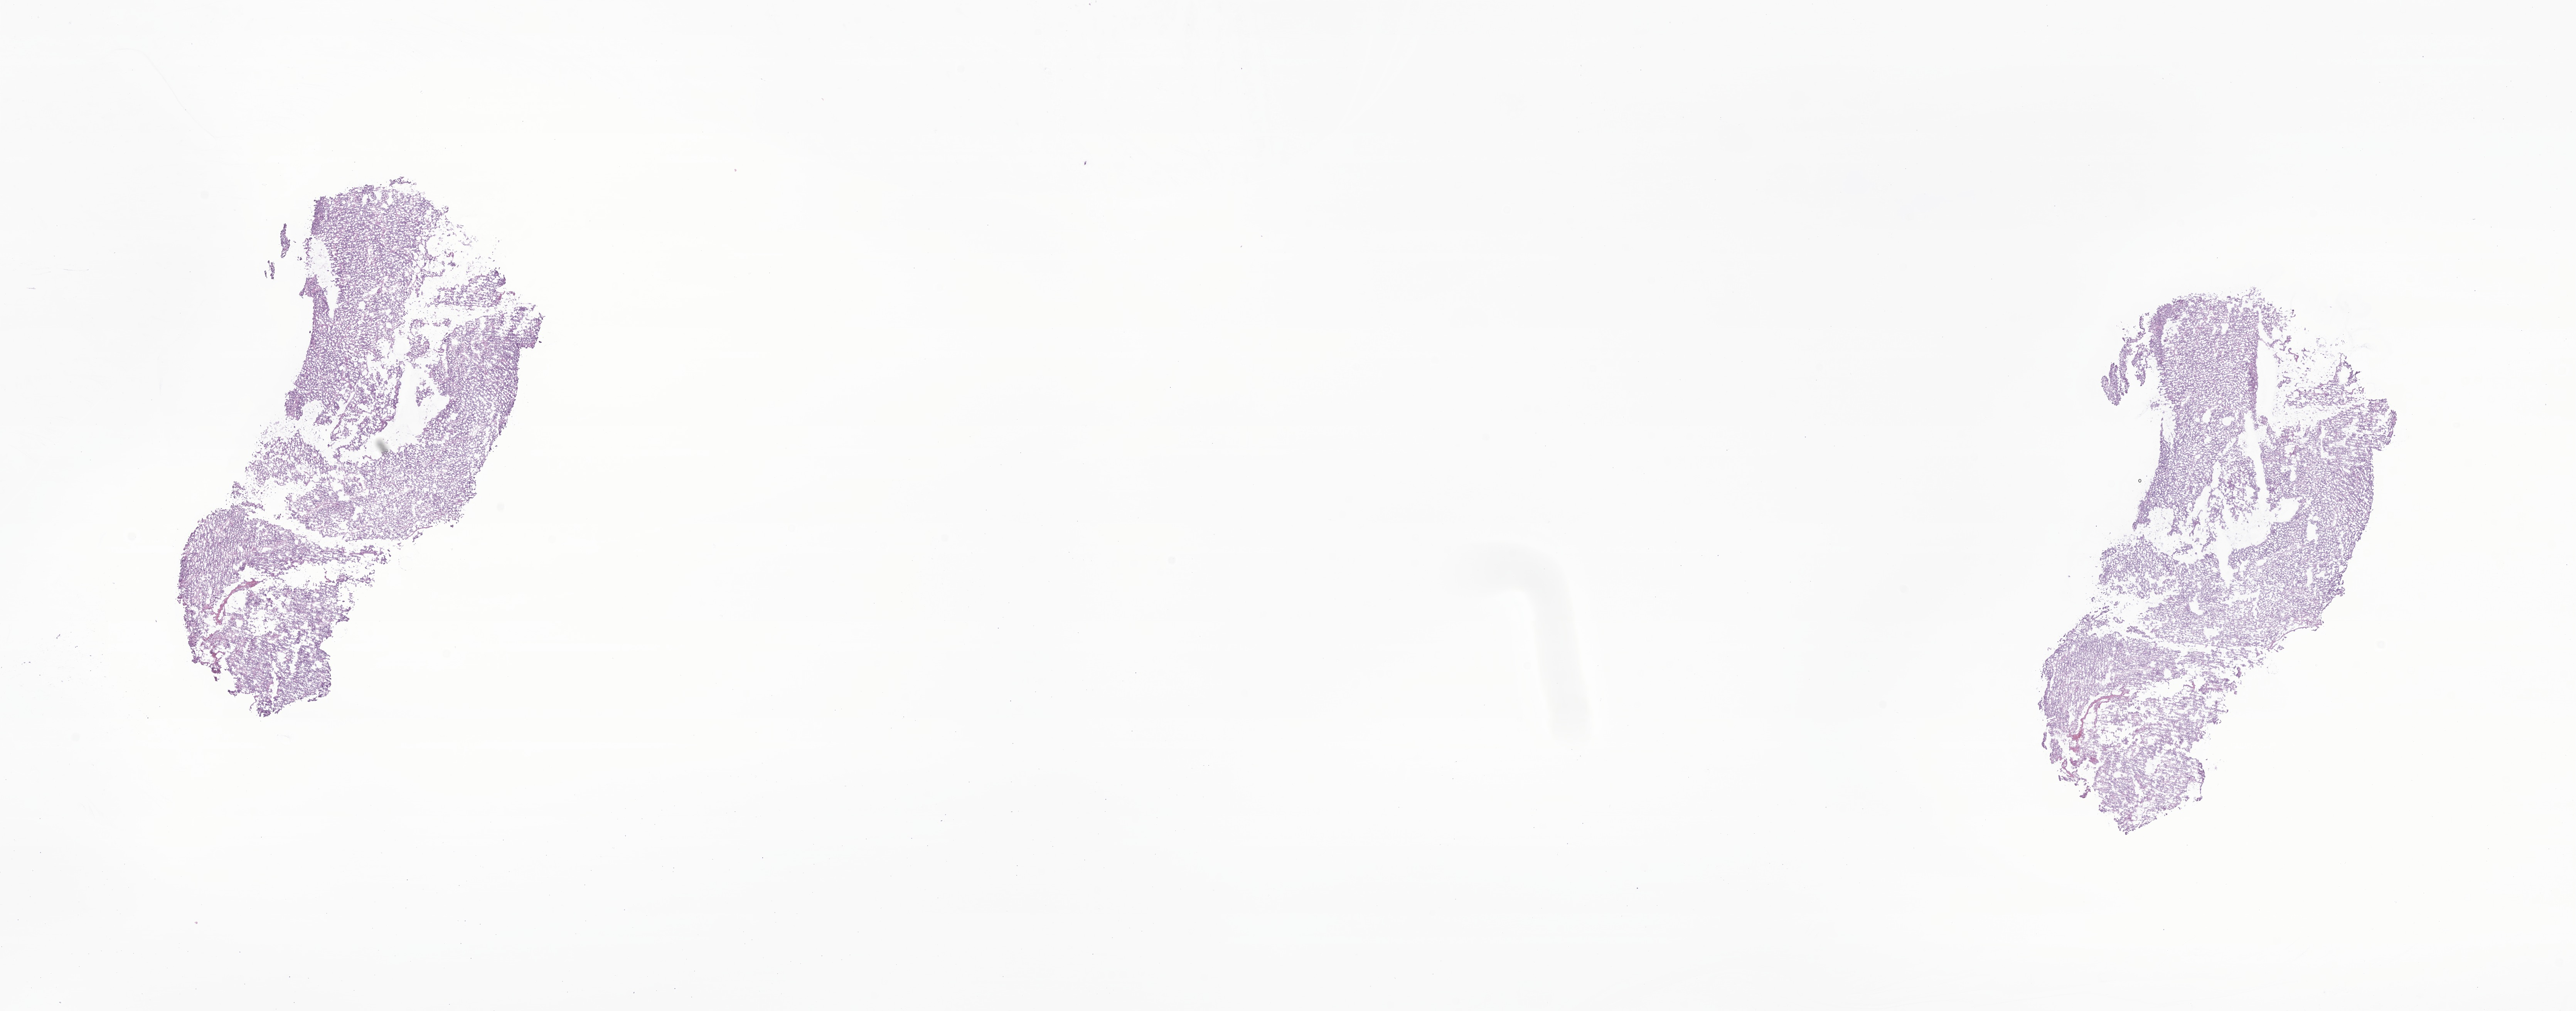
Digitized H&E-stained section of tumor tissue from the brain, low-resolution overview of the scanned area, about 28.2 x 11.1 mm. Frozen section (OCT-embedded). Patient male; age 200 months.
Diagnosis (ICD-O-3 morphology term): Neoplasm, uncertain whether benign or malignant.